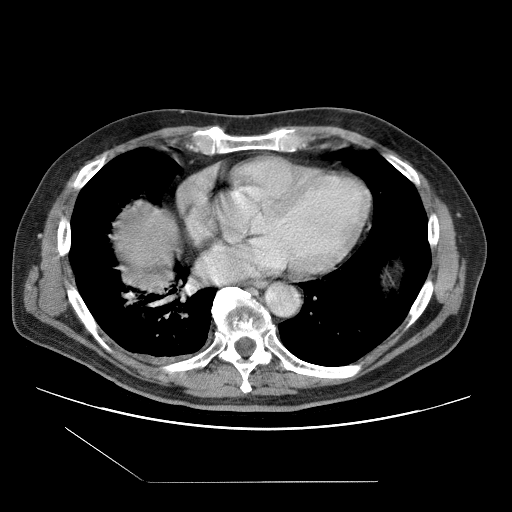
Contrast-enhanced abdominal CT (liver protocol), one axial slice. Position 103 of 109 along the scan axis. Reconstruction kernel STANDARD. 120 kVp. One of 2 acquisitions stored at this slice position. Soft-tissue window (W 400 / L 40 HU). 512 × 512 image matrix, field of view 400 × 400 mm. Case-level facts recorded for this patient, not image findings: diagnosis: hepatocellular carcinoma (patient treated with transarterial chemoembolisation; whether this scan precedes or follows treatment is not stated here); TNM stage (as recorded): Stage-IIIB; Child-Pugh class: A; tumour nodularity: multinodular.
Structures marked on this image (semi-automatic segmentation, software-assisted and operator-edited):
- liver parenchyma outside the tumour (the mass and vessels are separate outlines, so this box may not span the whole liver): bounding box [x1, y1, x2, y2] px = [114, 202, 178, 274]